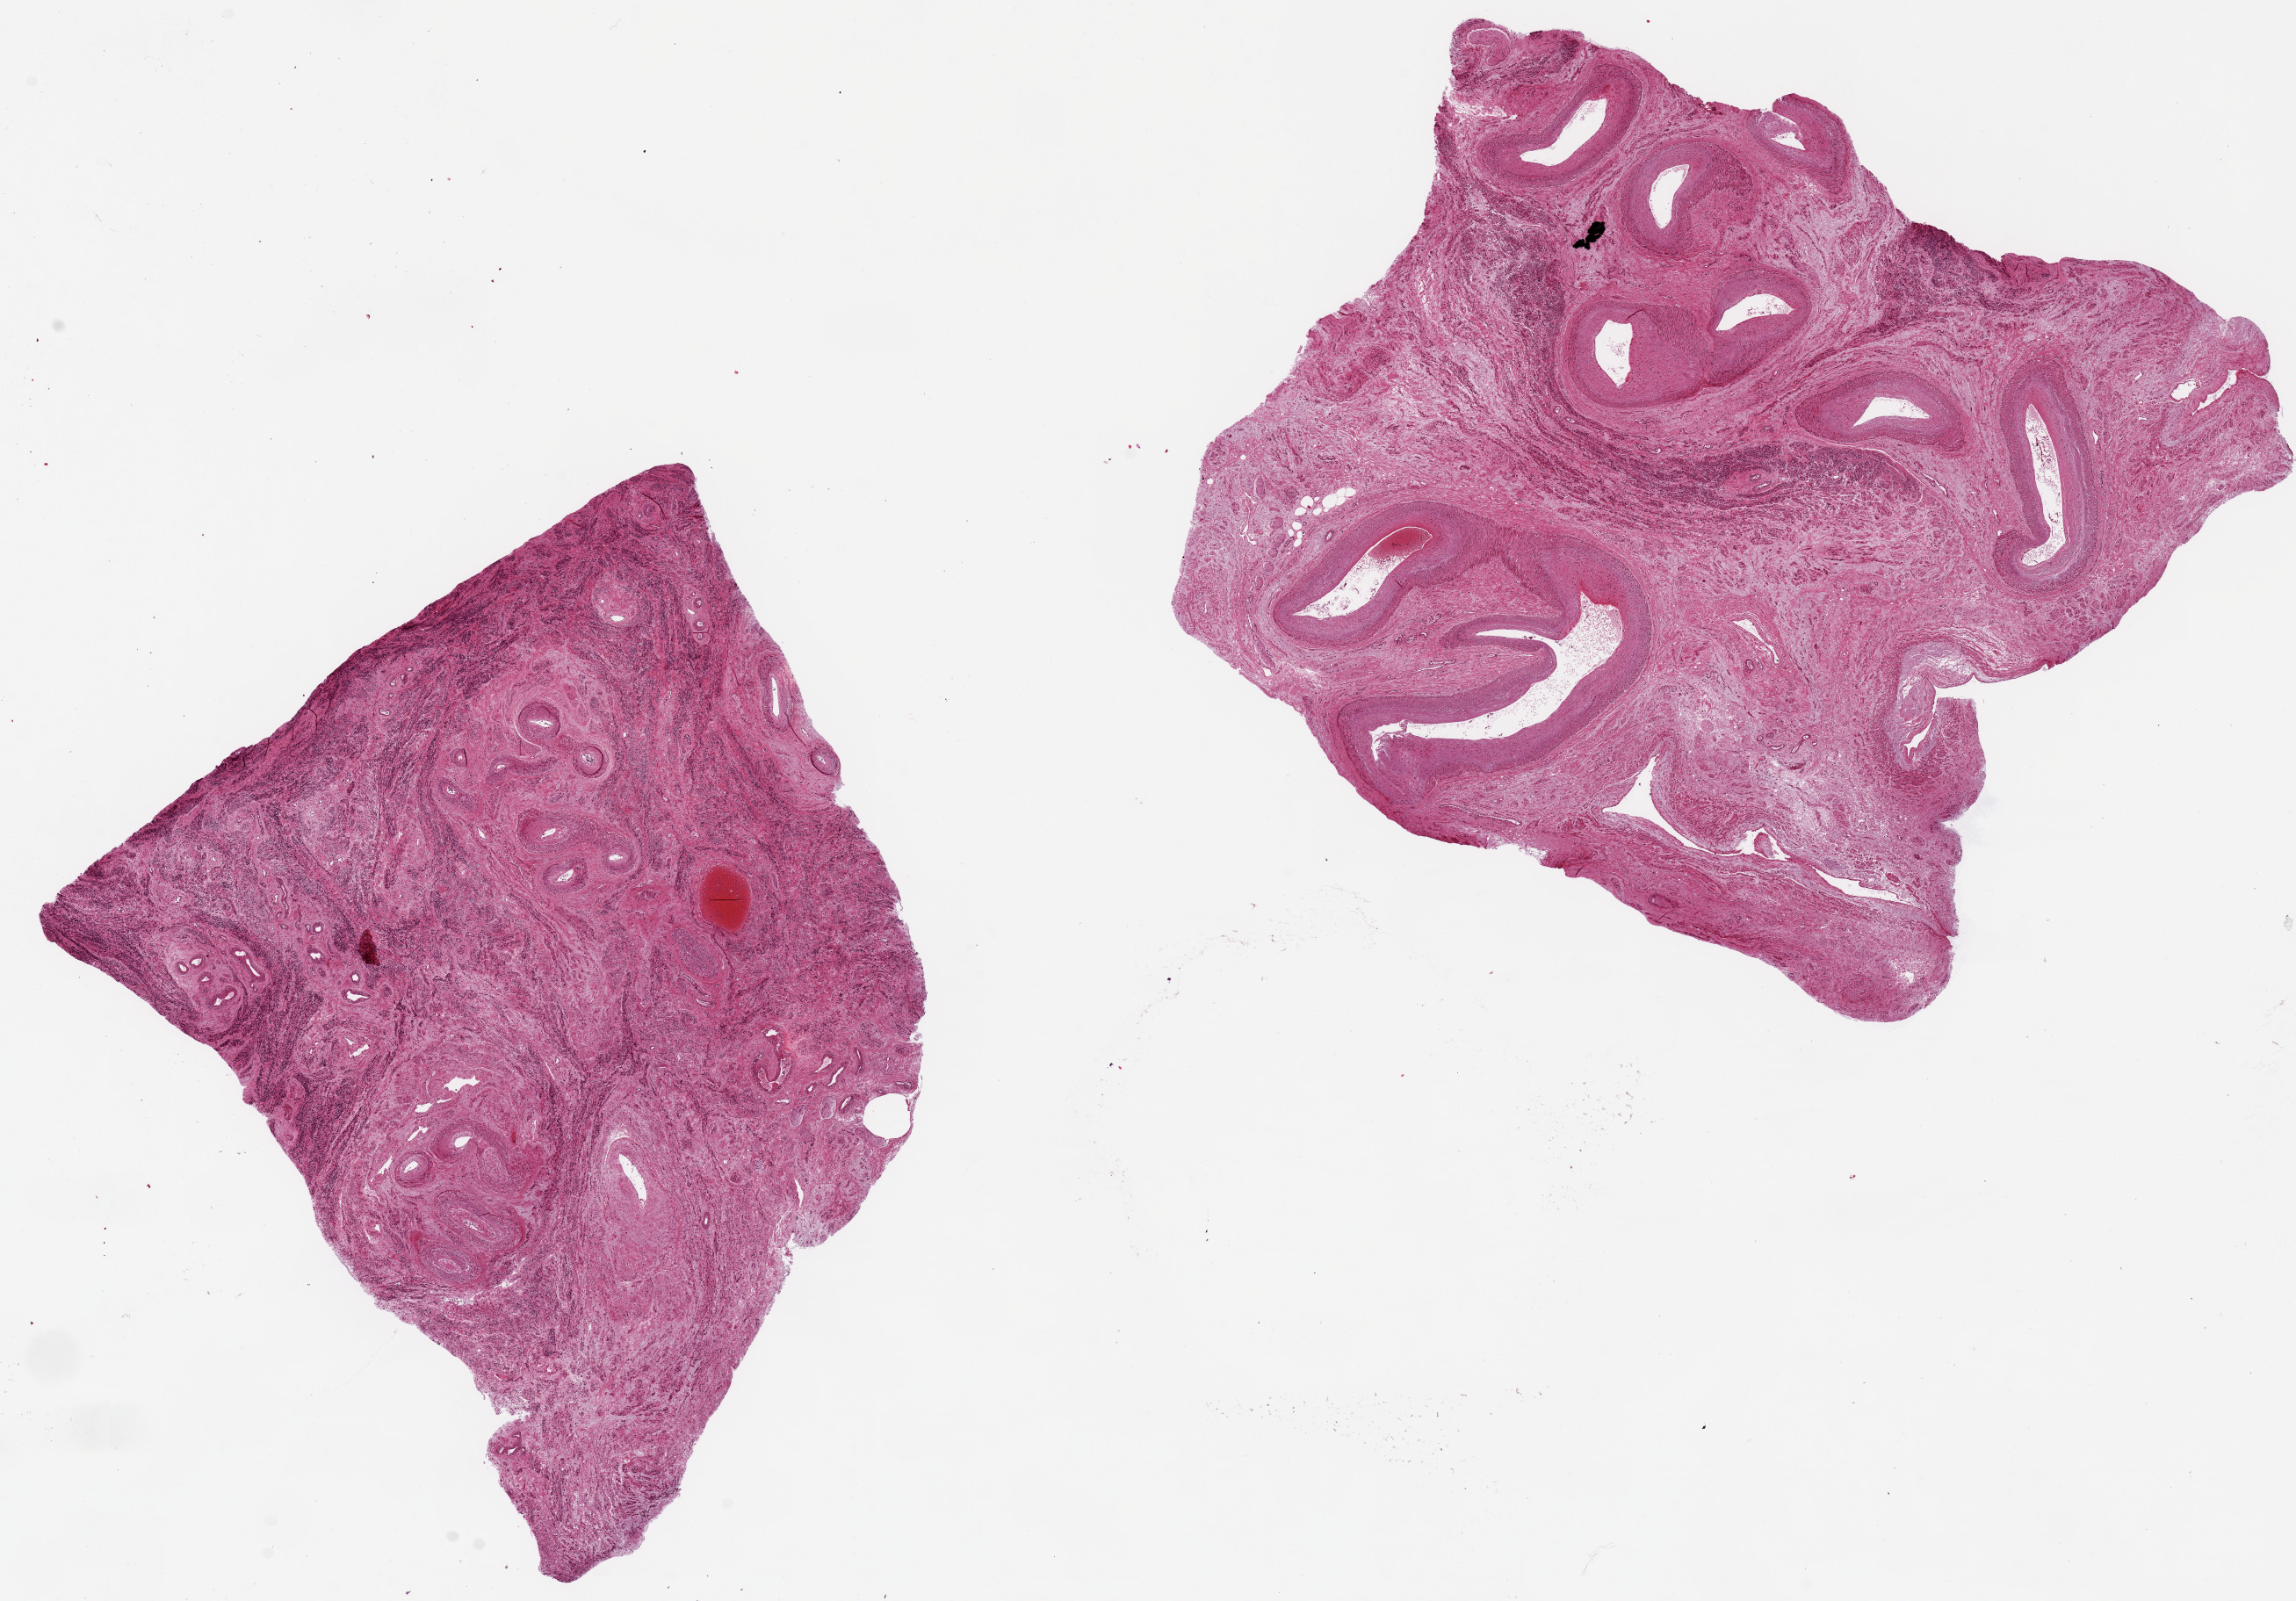
Haematoxylin and eosin whole-slide image, a low-resolution overview of the entire scanned area, about 20.7 x 14.4 mm. PAXgene-fixed paraffin-embedded (PFPE) section. Sampled site (target tissue): uterus. Tissue donor sample. Female donor.
Pathologist's review note for this sample: 2 pieces, 8x7 & 8x7mm; prominent subserosal vessels, one, no endometrum.